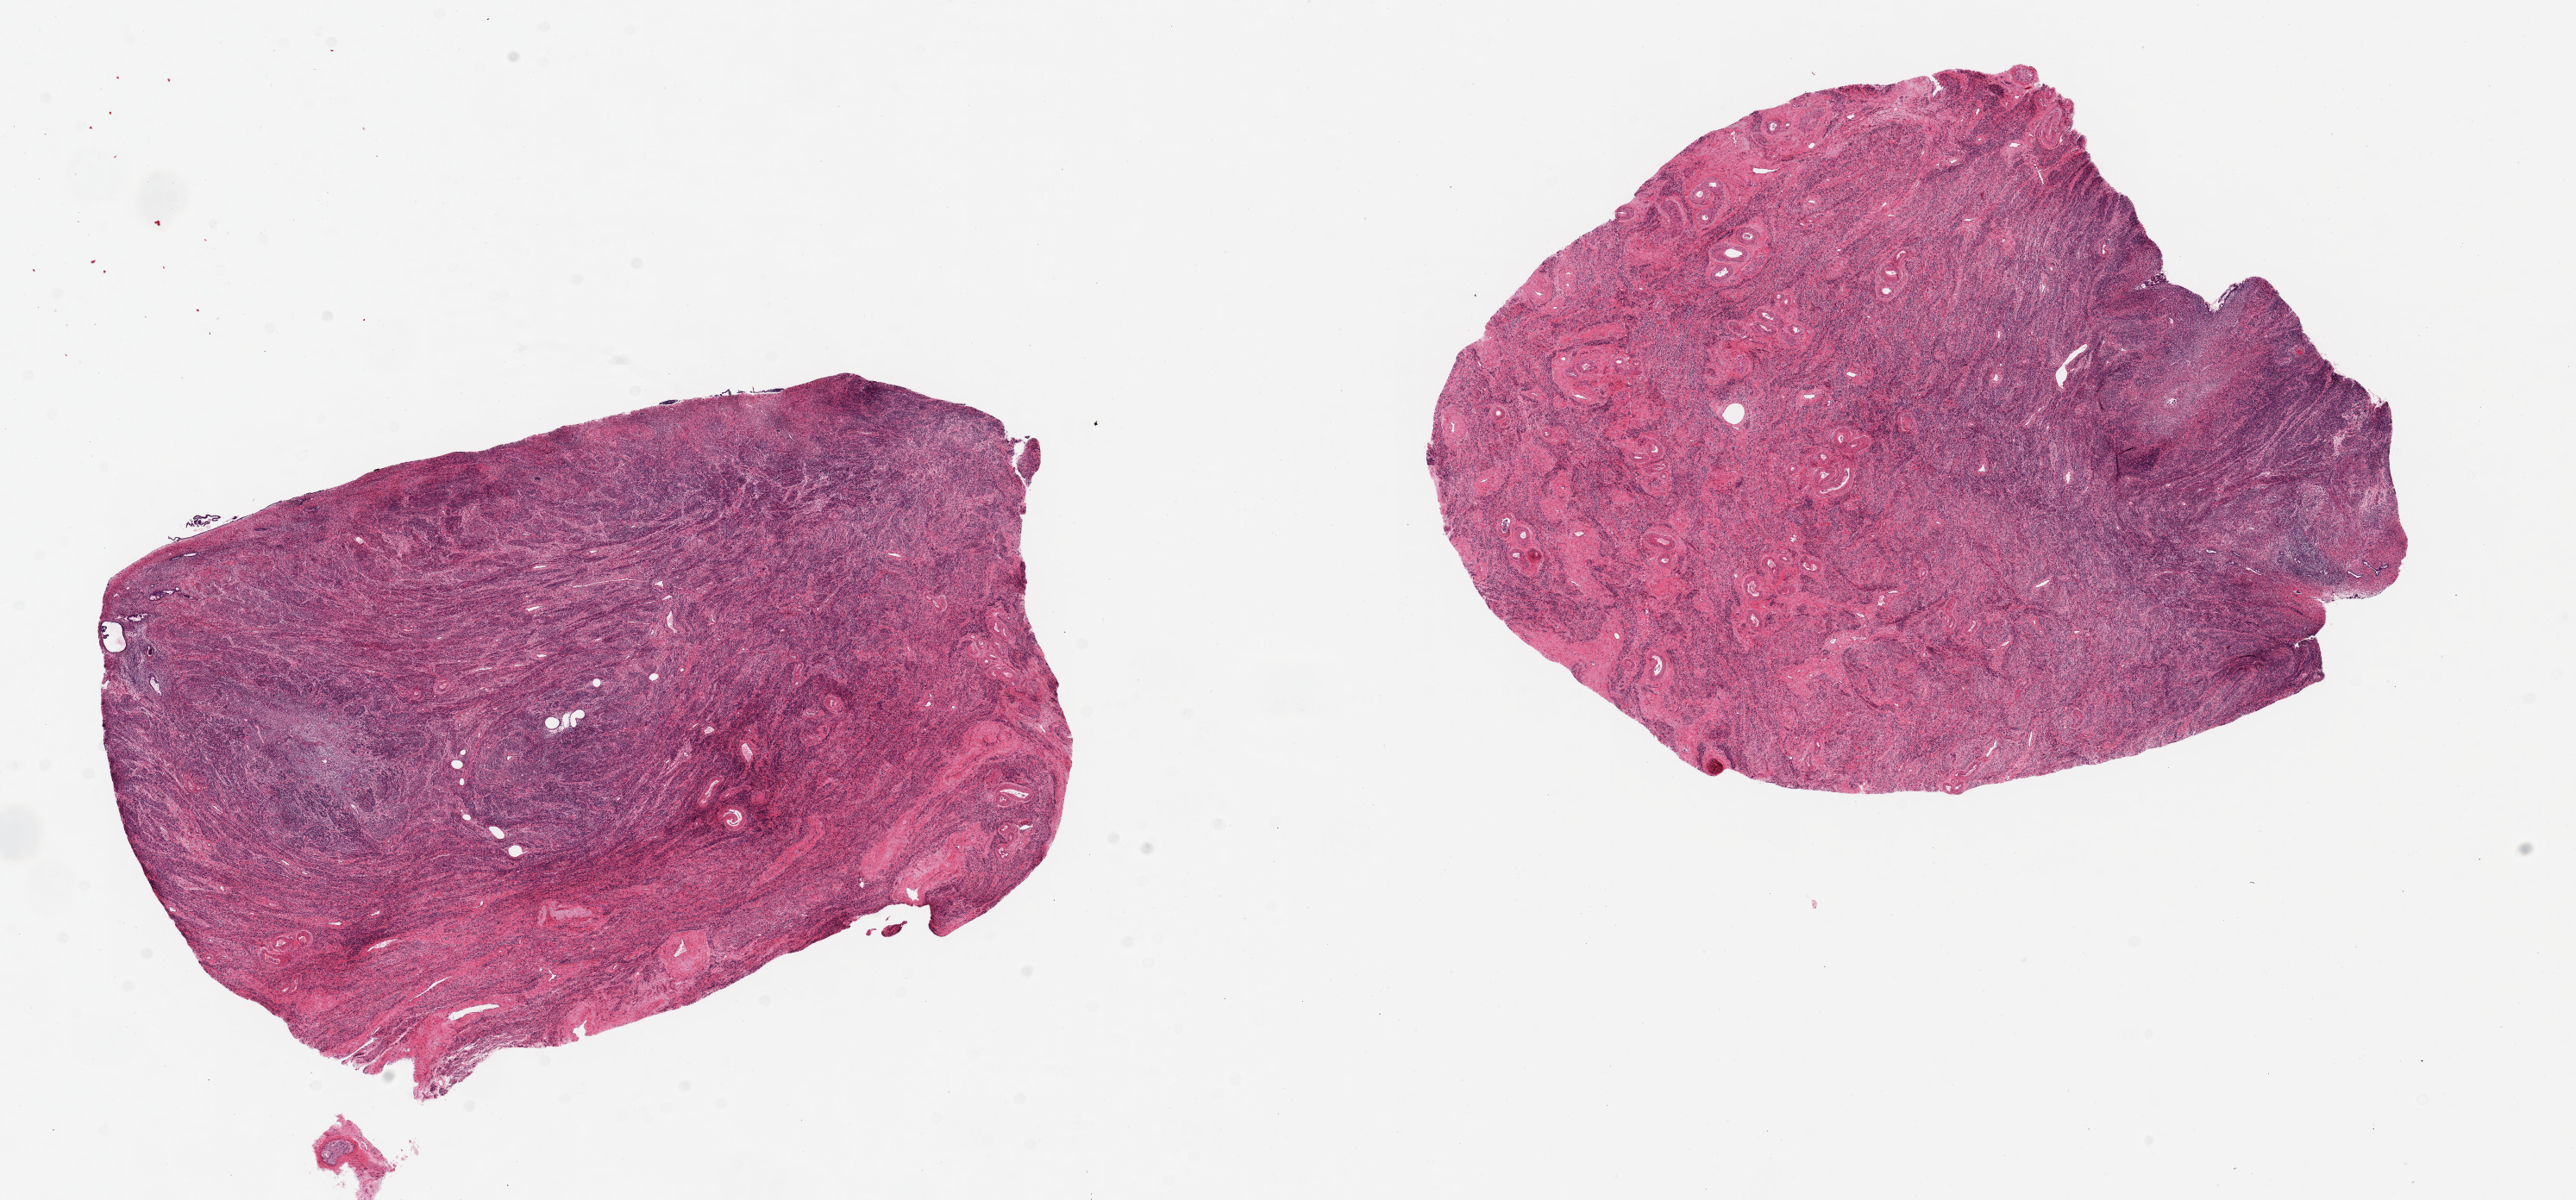
Haematoxylin and eosin whole-slide image — shown as a low-resolution overview of the whole scanned area (about 23.6 x 11.0 mm), PAXgene-fixed, paraffin-embedded tissue, section of uterus (target tissue), donor tissue sample. Donor sex: female.
Reviewer comment on this tissue sample: 2 pieces, 9x6 & 9x6mm; myometrium and atrophic endometrium with small foci of glands.